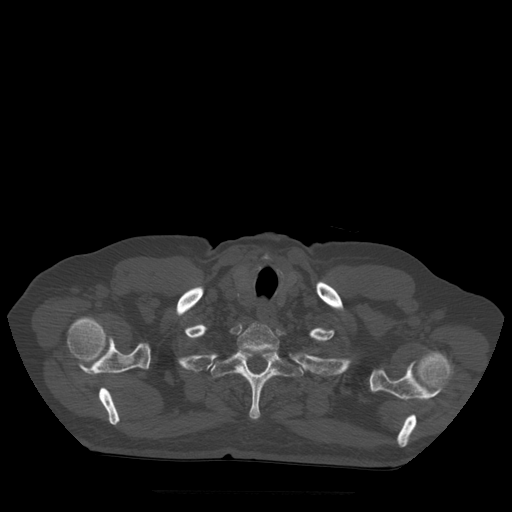
CT including the spine, one axial slice; slice 430 of 522 in the series (ordered by position); bone window (W 1800 / L 400 HU); 512 × 512 image matrix, field of view 420 × 420 mm. Patient age 72 years. From the clinical record (not read from this slice): primary cancer: prostate.
Structures marked on this image (semi-automatically segmented with operator editing):
- T1 vertebra: bounding box (x1, y1, x2, y2) in pixels: (238, 324, 280, 352)
- T2 vertebra: (211, 349, 304, 420)